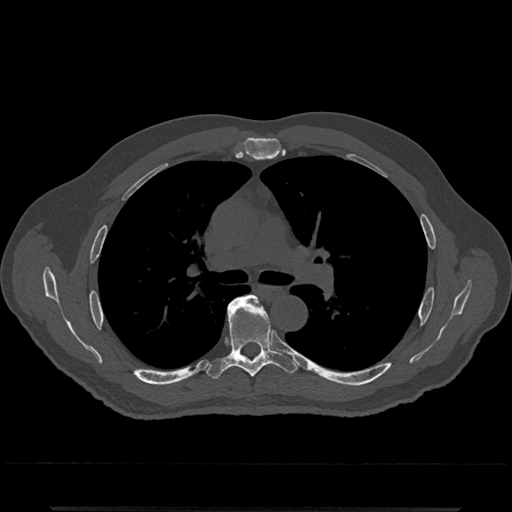
CT including the spine, one axial slice; reconstruction kernel Br40s/3; 120 kVp; bone window (W 1800 / L 400 HU); 0.5 mm slice thickness; 512 × 512 image matrix. Male patient, age 67 years. Case-level facts recorded for this patient, not image findings: primary cancer: prostate.
Outlined on this slice (semi-automatically segmented with operator editing):
- T5 vertebra: bounding box [x1, y1, x2, y2] px = [244, 296, 263, 309]
- T6 vertebra: [206, 295, 298, 378]